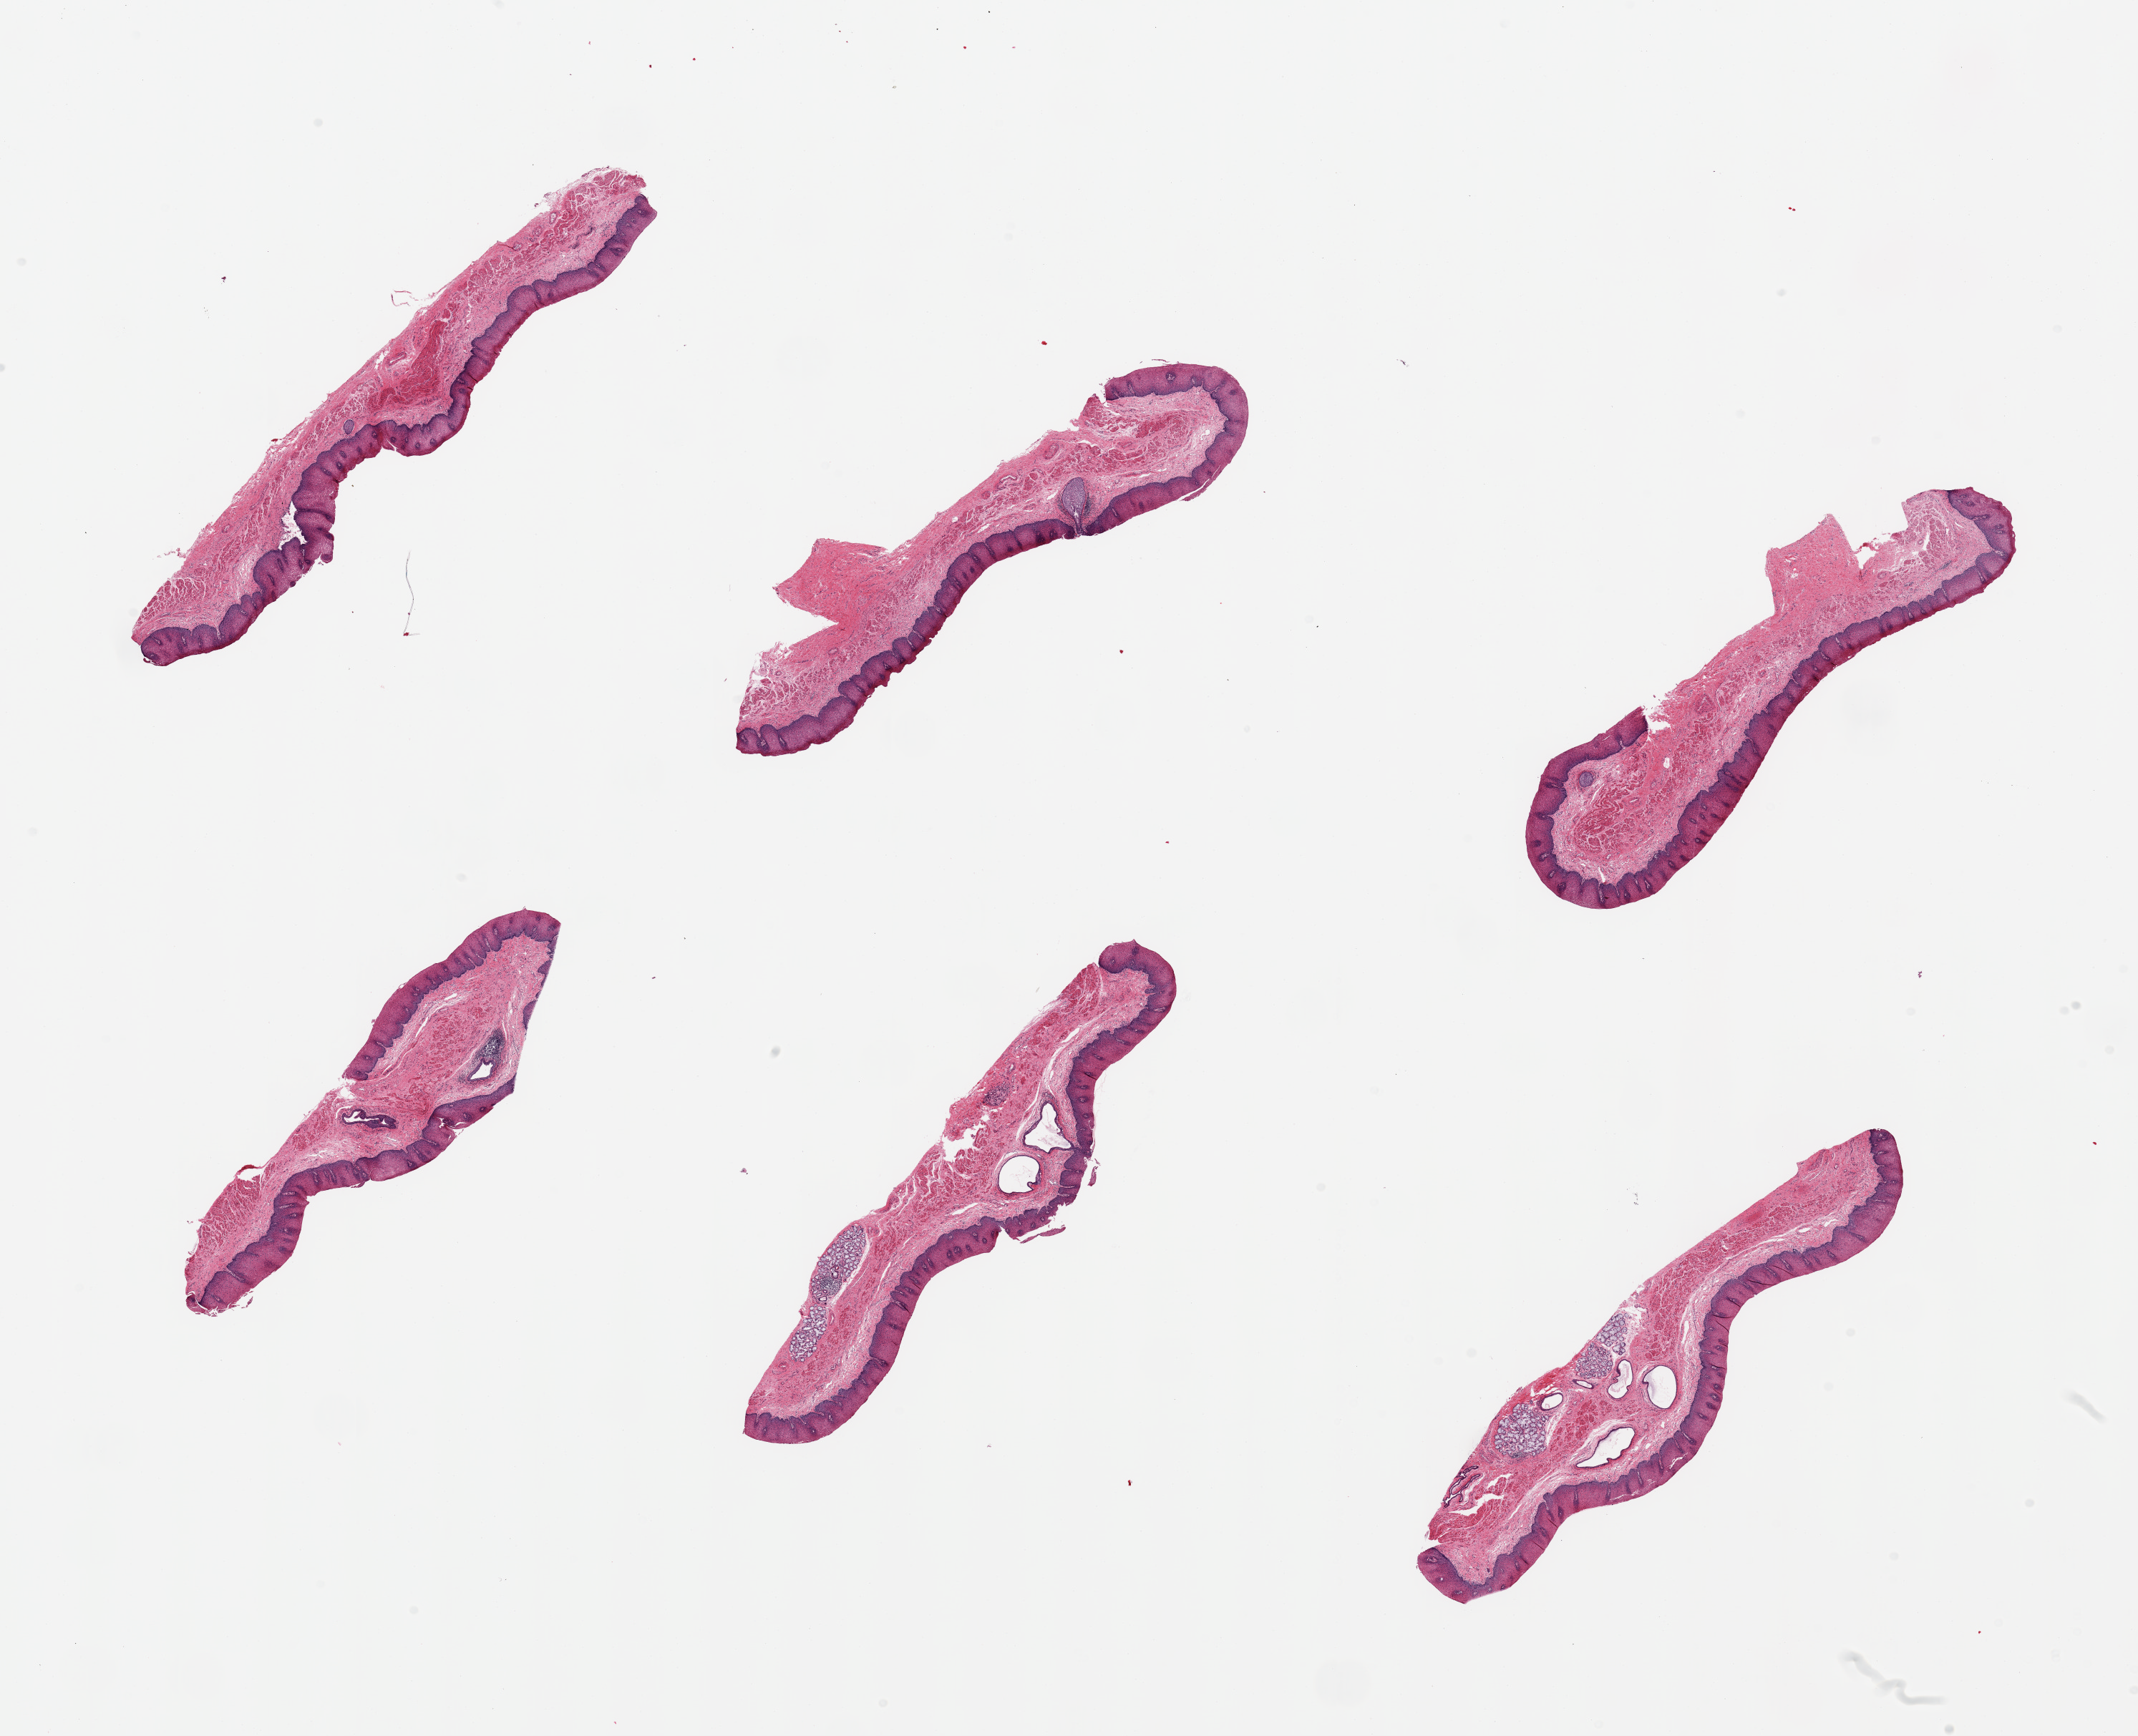
Digitized hematoxylin and eosin (H&E)-stained section, low-resolution overview of the scanned area, about 23.6 x 19.2 mm. PAXgene-fixed, paraffin-embedded tissue. Section of esophageal mucous membrane (target tissue). Donor tissue sample. Donor: male.
• reviewer comment on this tissue sample: 6 pieces, squamousmucosa is ~0.3mm, 25-30% thickness; a few submucosal mucus glands present